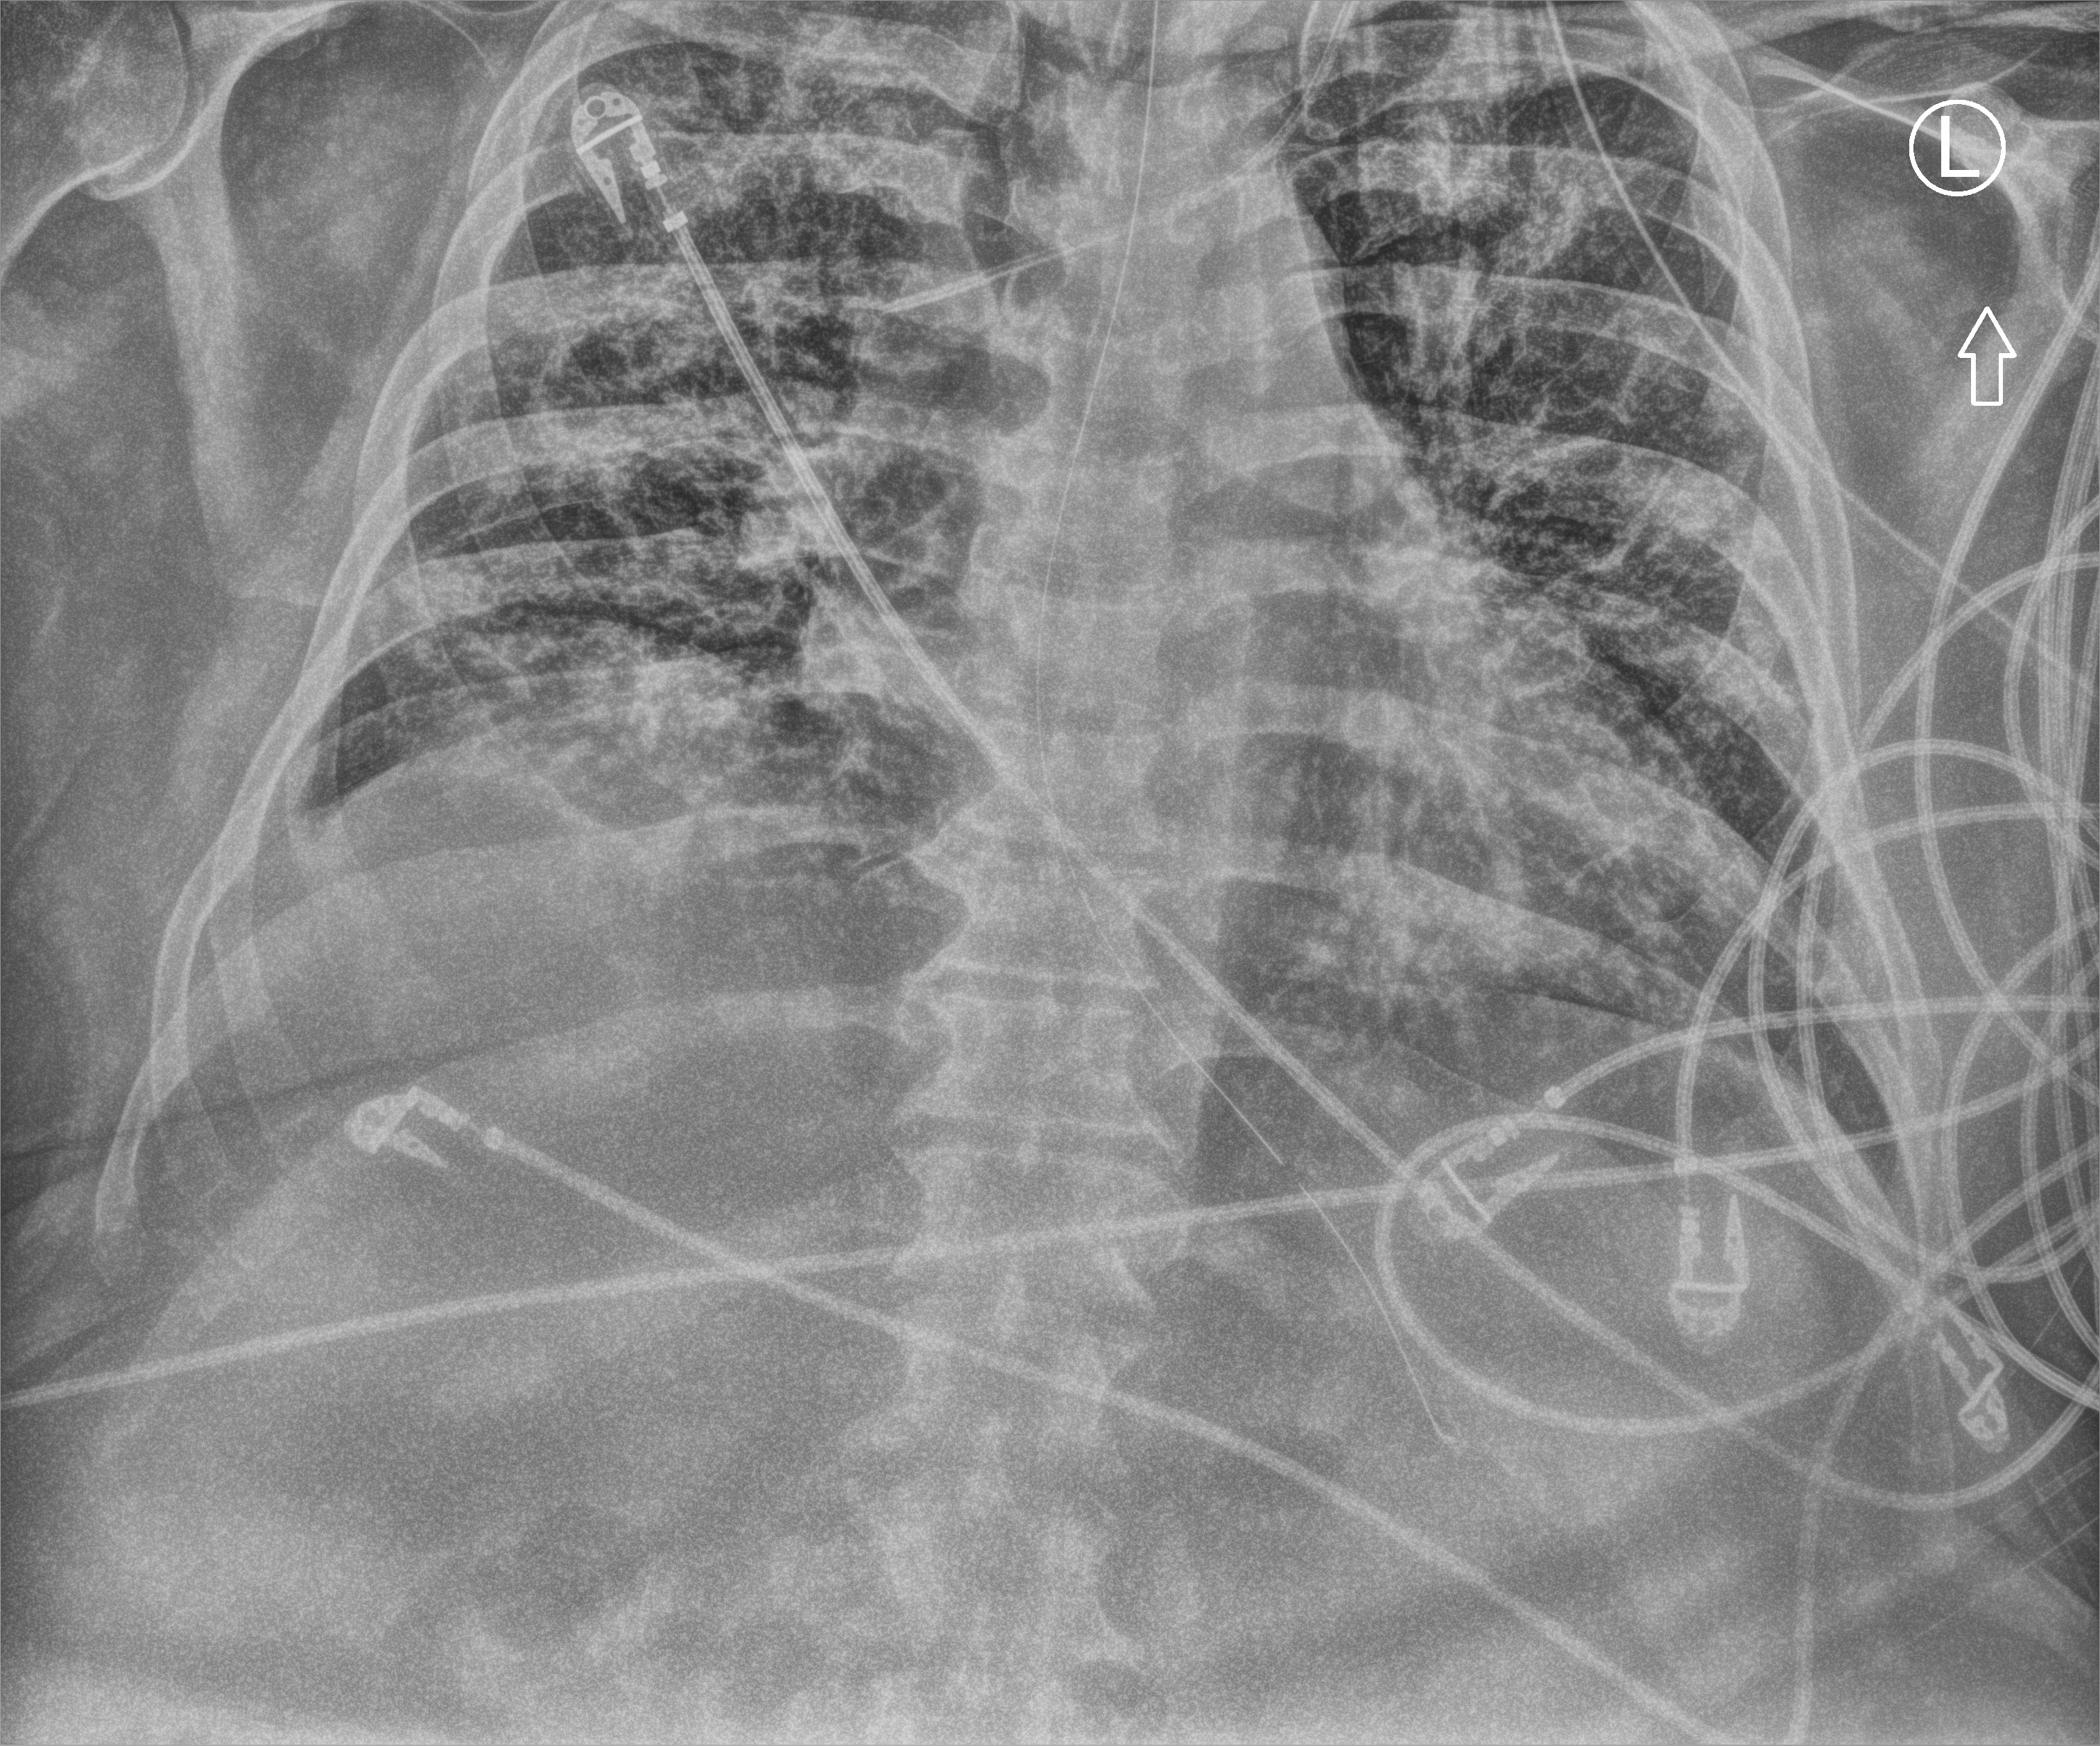
Chest X-ray (portable); anteroposterior (AP) projection. Male patient hospitalised with COVID-19, age 18–59 years.
From the hospital-stay record, not from the radiograph (when in the stay this image was taken is not recorded): admitted to intensive care during this hospital stay: yes; diabetes (admission record): no; chronic kidney disease (admission record): no.